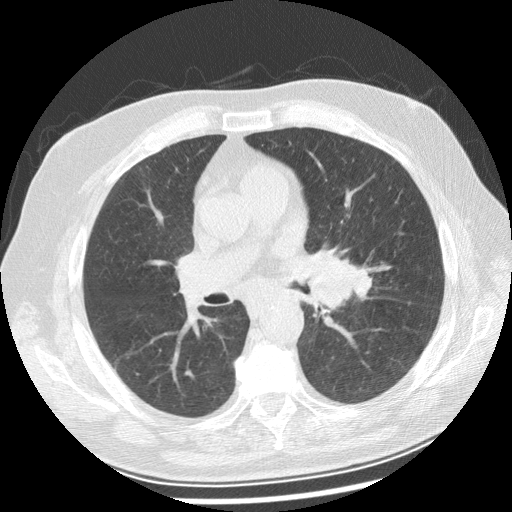
Low-dose screening chest CT, one axial slice; slice 140 of 250 in the series (ordered by position); lung window (W 1500 / L -600 HU); 512 × 512 image matrix, field of view 360 × 360 mm.
Structures marked on this image (manually delineated by an expert):
- lesion 1 (tumor, left main bronchus): bounding box [x1, y1, x2, y2] px = [308, 262, 373, 309]